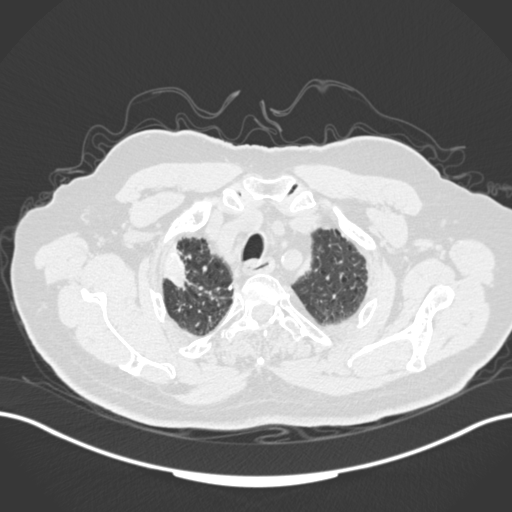
Chest CT, one axial slice; position 147 of 205 along the scan axis; 120 kVp; lung window (W 1500 / L -600 HU); 1 mm slice thickness; 512 × 512 image matrix. Patient: male, 72 years. Case-level facts recorded for this patient, not image findings: clinical TNM (as recorded): T1a N0 M0.
Annotated regions visible in this slice (rectangle marked by the reading radiologist):
- lung tumour (recorded histology: squamous cell carcinoma): bounding box (x1, y1, x2, y2) in pixels: (160, 239, 197, 286)